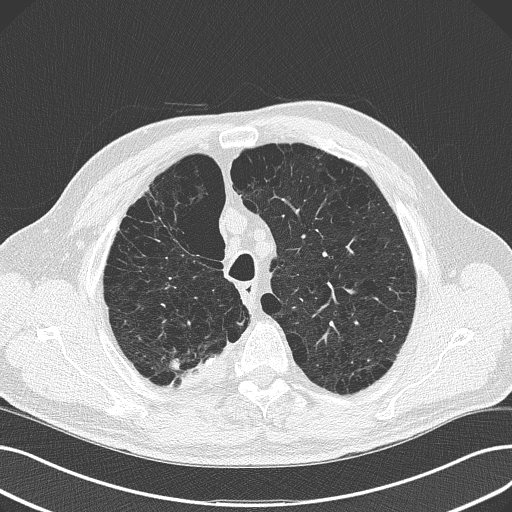
Axial slice from a low-dose chest CT screening exam; second annual screen; lung window (W 1500 / L -600 HU); 2 mm slice thickness; lung (sharp) reconstruction kernel (B50f); 120 kVp; slice 43 of 165 in the series. Male, age 68 years at enrolment.
Expert reader's lesion annotation, bounding box (x1, y1, x2, y2) in pixels: (143, 332, 231, 398). The screening reader recorded 4 non-calcified nodules or masses ≥4 mm on this exam; which of them this box marks is not recorded. Official screen result: positive, other. Later outcome: lung cancer diagnosed 304 days after this screen — adenocarcinoma, NOS, right upper lobe, stage IV (AJCC 6th edition), 29 mm at pathology.